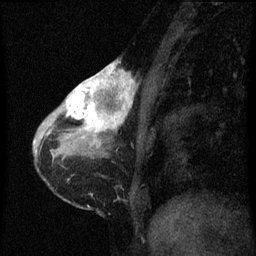
Breast MRI (dynamic contrast-enhanced), one sagittal slice; slice 19 of 60 in the series (ordered by position); dynamic contrast-enhanced series, image 2 of 3 at this slice position (ordered by acquisition); 1.5 T; TE 4.2 ms, TR 8 ms; 2 mm slice thickness; 256 × 256 image matrix, field of view 180 × 180 mm. Patient: female, 38 years.
Annotated regions visible in this slice (semi-automatically segmented with operator editing):
- analysis volume of interest (the breast-tissue region the enhancement analysis was run in; not a lesion): bounding box (x1, y1, x2, y2) in pixels: (61, 62, 136, 147)
- tumour enhancement mask (voxels above the 70 % enhancement threshold inside the analysis volume of interest): (65, 62, 136, 145)